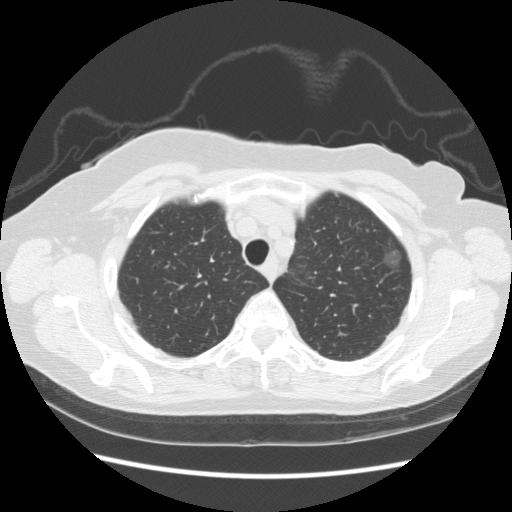
Axial slice from a low-dose chest CT screening exam. Baseline screening round. Lung window (W 1500 / L -600 HU). 2.5 mm slice thickness. Slice 35 of 247 in the series. Female, age 73 years at enrolment. Former smoker at enrolment.
- Expert reader's lesion annotation, box from (x=372, y=230) to (x=414, y=276) px.
- The screening reader recorded 3 non-calcified nodules or masses ≥4 mm on this exam; which of them this box marks is not recorded.
- Official screen result: positive, change unspecified: nodule(s) >= 4 mm or enlarging nodule(s), mass(es), or other non-specific abnormalities suspicious for lung cancer.
- Later outcome: lung cancer diagnosed 445 days after this screen — bronchiolo-alveolar adenocarcinoma, NOS, left upper lobe, well differentiated (G1), stage IA (AJCC 6th edition), 10 mm at pathology.